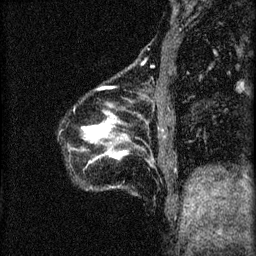
Breast MRI (dynamic contrast-enhanced), one sagittal slice; position 11 of 60 along the scan axis; 3 images stored at this slice position (order not interpretable as contrast timing); 1.5 T; TE 4.2 ms, TR 8.2 ms; 256 × 256 image matrix. Female patient, age 40 years.
Annotated regions visible in this slice (semi-automatically segmented with operator editing):
- analysis volume of interest (the breast-tissue region the enhancement analysis was run in; not a lesion): box from (x=70, y=88) to (x=173, y=189) px
- tumour enhancement mask (voxels above the 70 % enhancement threshold inside the analysis volume of interest): (x=82, y=90)–(x=127, y=159)